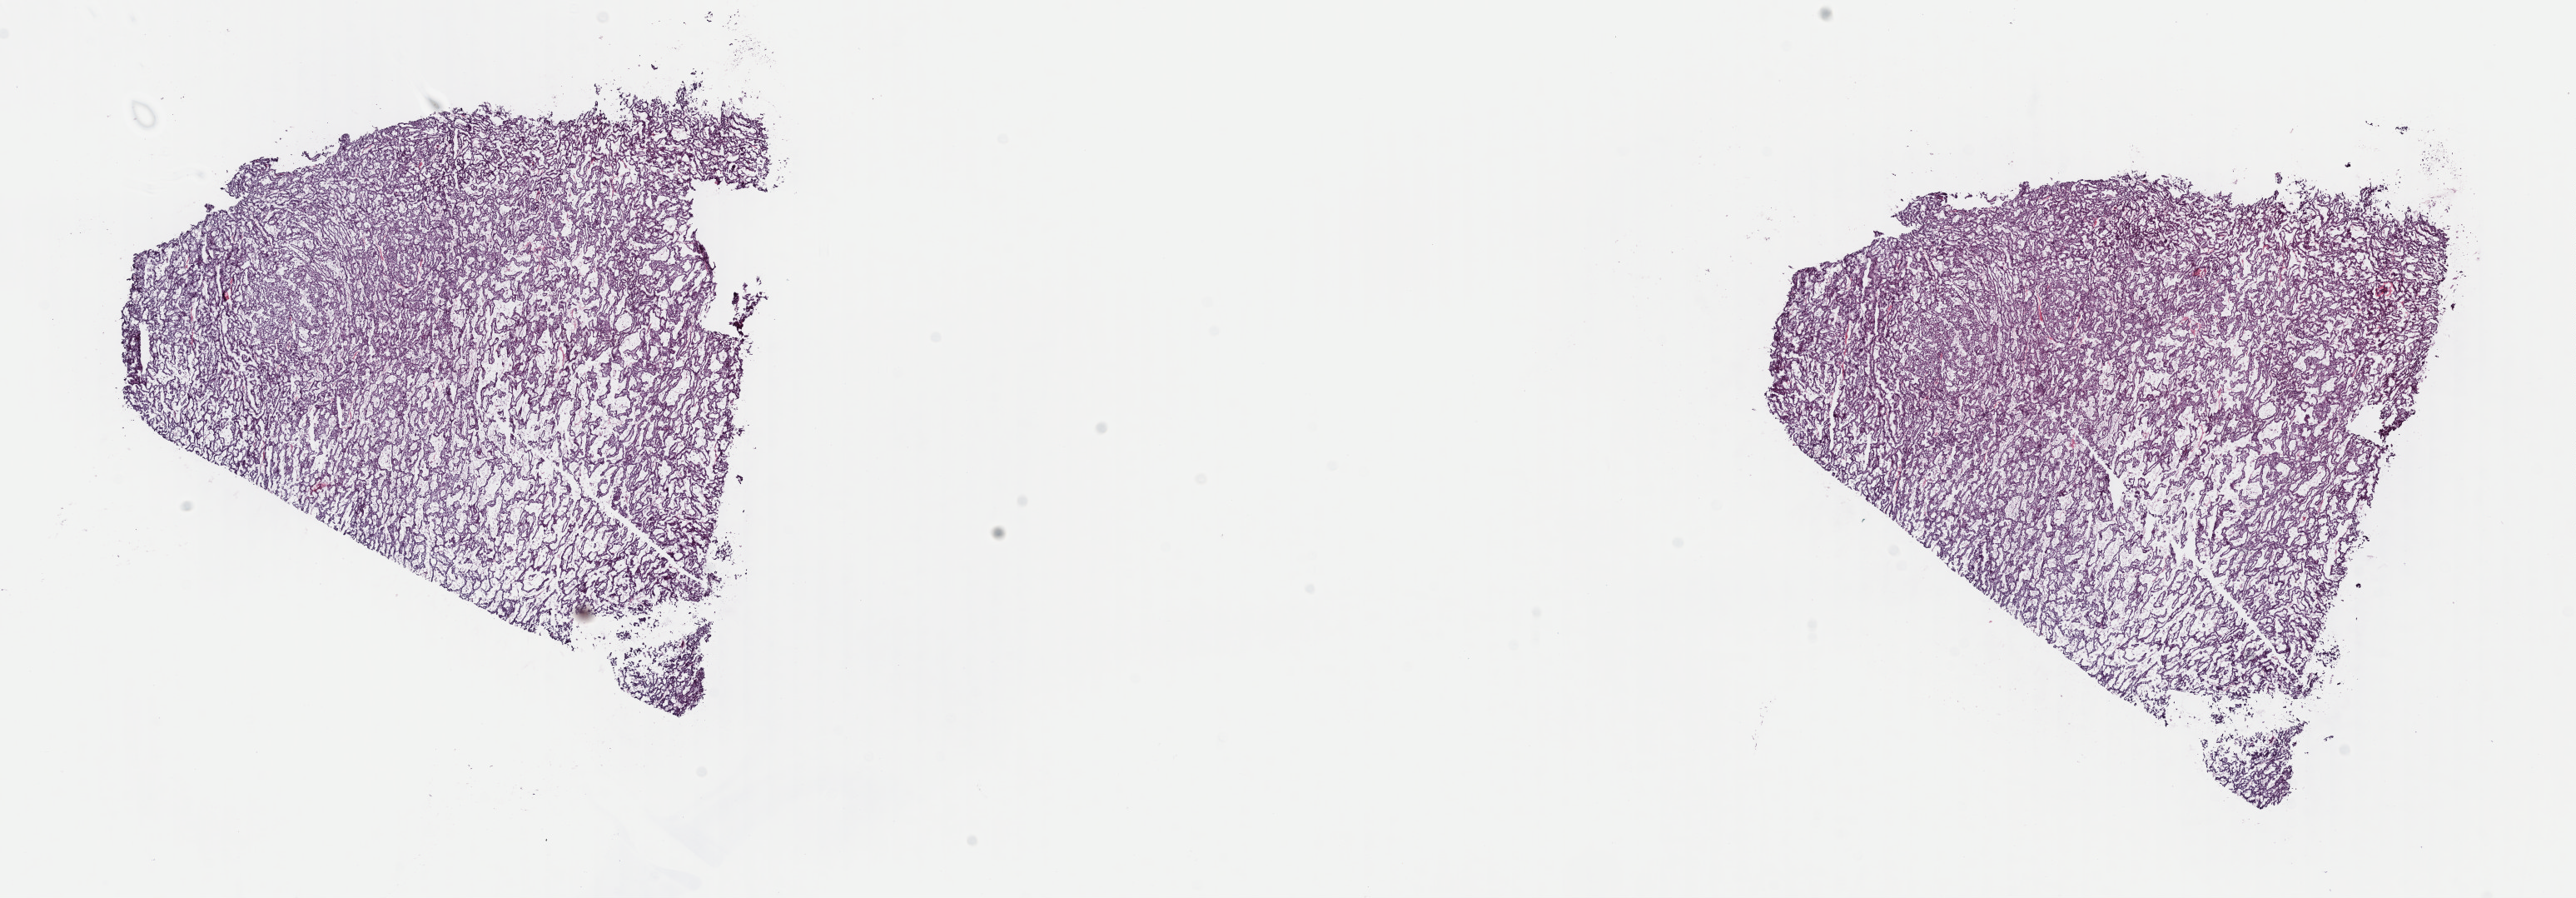
Whole-slide histology image, Hematoxylin and eosin (H&E) stained — shown as a low-resolution overview of the whole scanned area (about 24.4 x 8.5 mm). Frozen section. Sample: primary tumour, kidney. Patient: male, age at initial diagnosis 65 years. Composition of this section per pathologist review: tumour cells 80%, tumour nuclei 90%, normal cells 0%, stromal cells 20%, necrosis 0%. Inflammatory infiltration, as recorded: lymphocyte infiltration 0%, monocyte infiltration 0%, neutrophil infiltration 0%.
• TNM: T1b NX MX
• histologic diagnosis: Papillary adenocarcinoma, NOS
• laterality: right
• AJCC pathologic stage: I (7th edition)